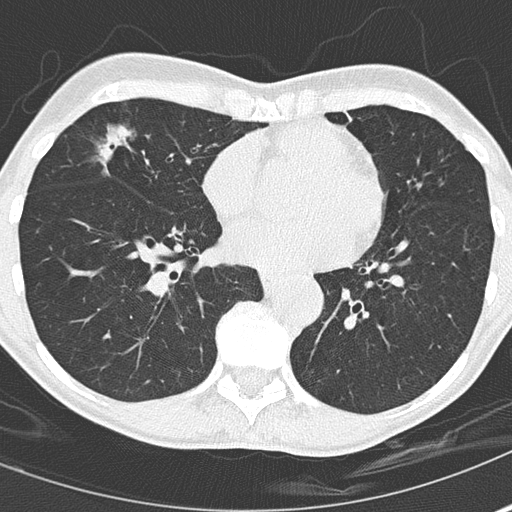
Chest CT (low-dose screening protocol), one axial image, second annual screen, lung window (W 1500 / L -600 HU), lung (sharp) reconstruction kernel (B50f). Female, age 67 years at enrolment. Current smoker at enrolment.
Expert reader's lesion annotation, box from (x=83, y=112) to (x=187, y=202) px. The screening reader recorded 2 non-calcified nodules or masses ≥4 mm on this exam; which of them this box marks is not recorded. Official screen result: positive, other.